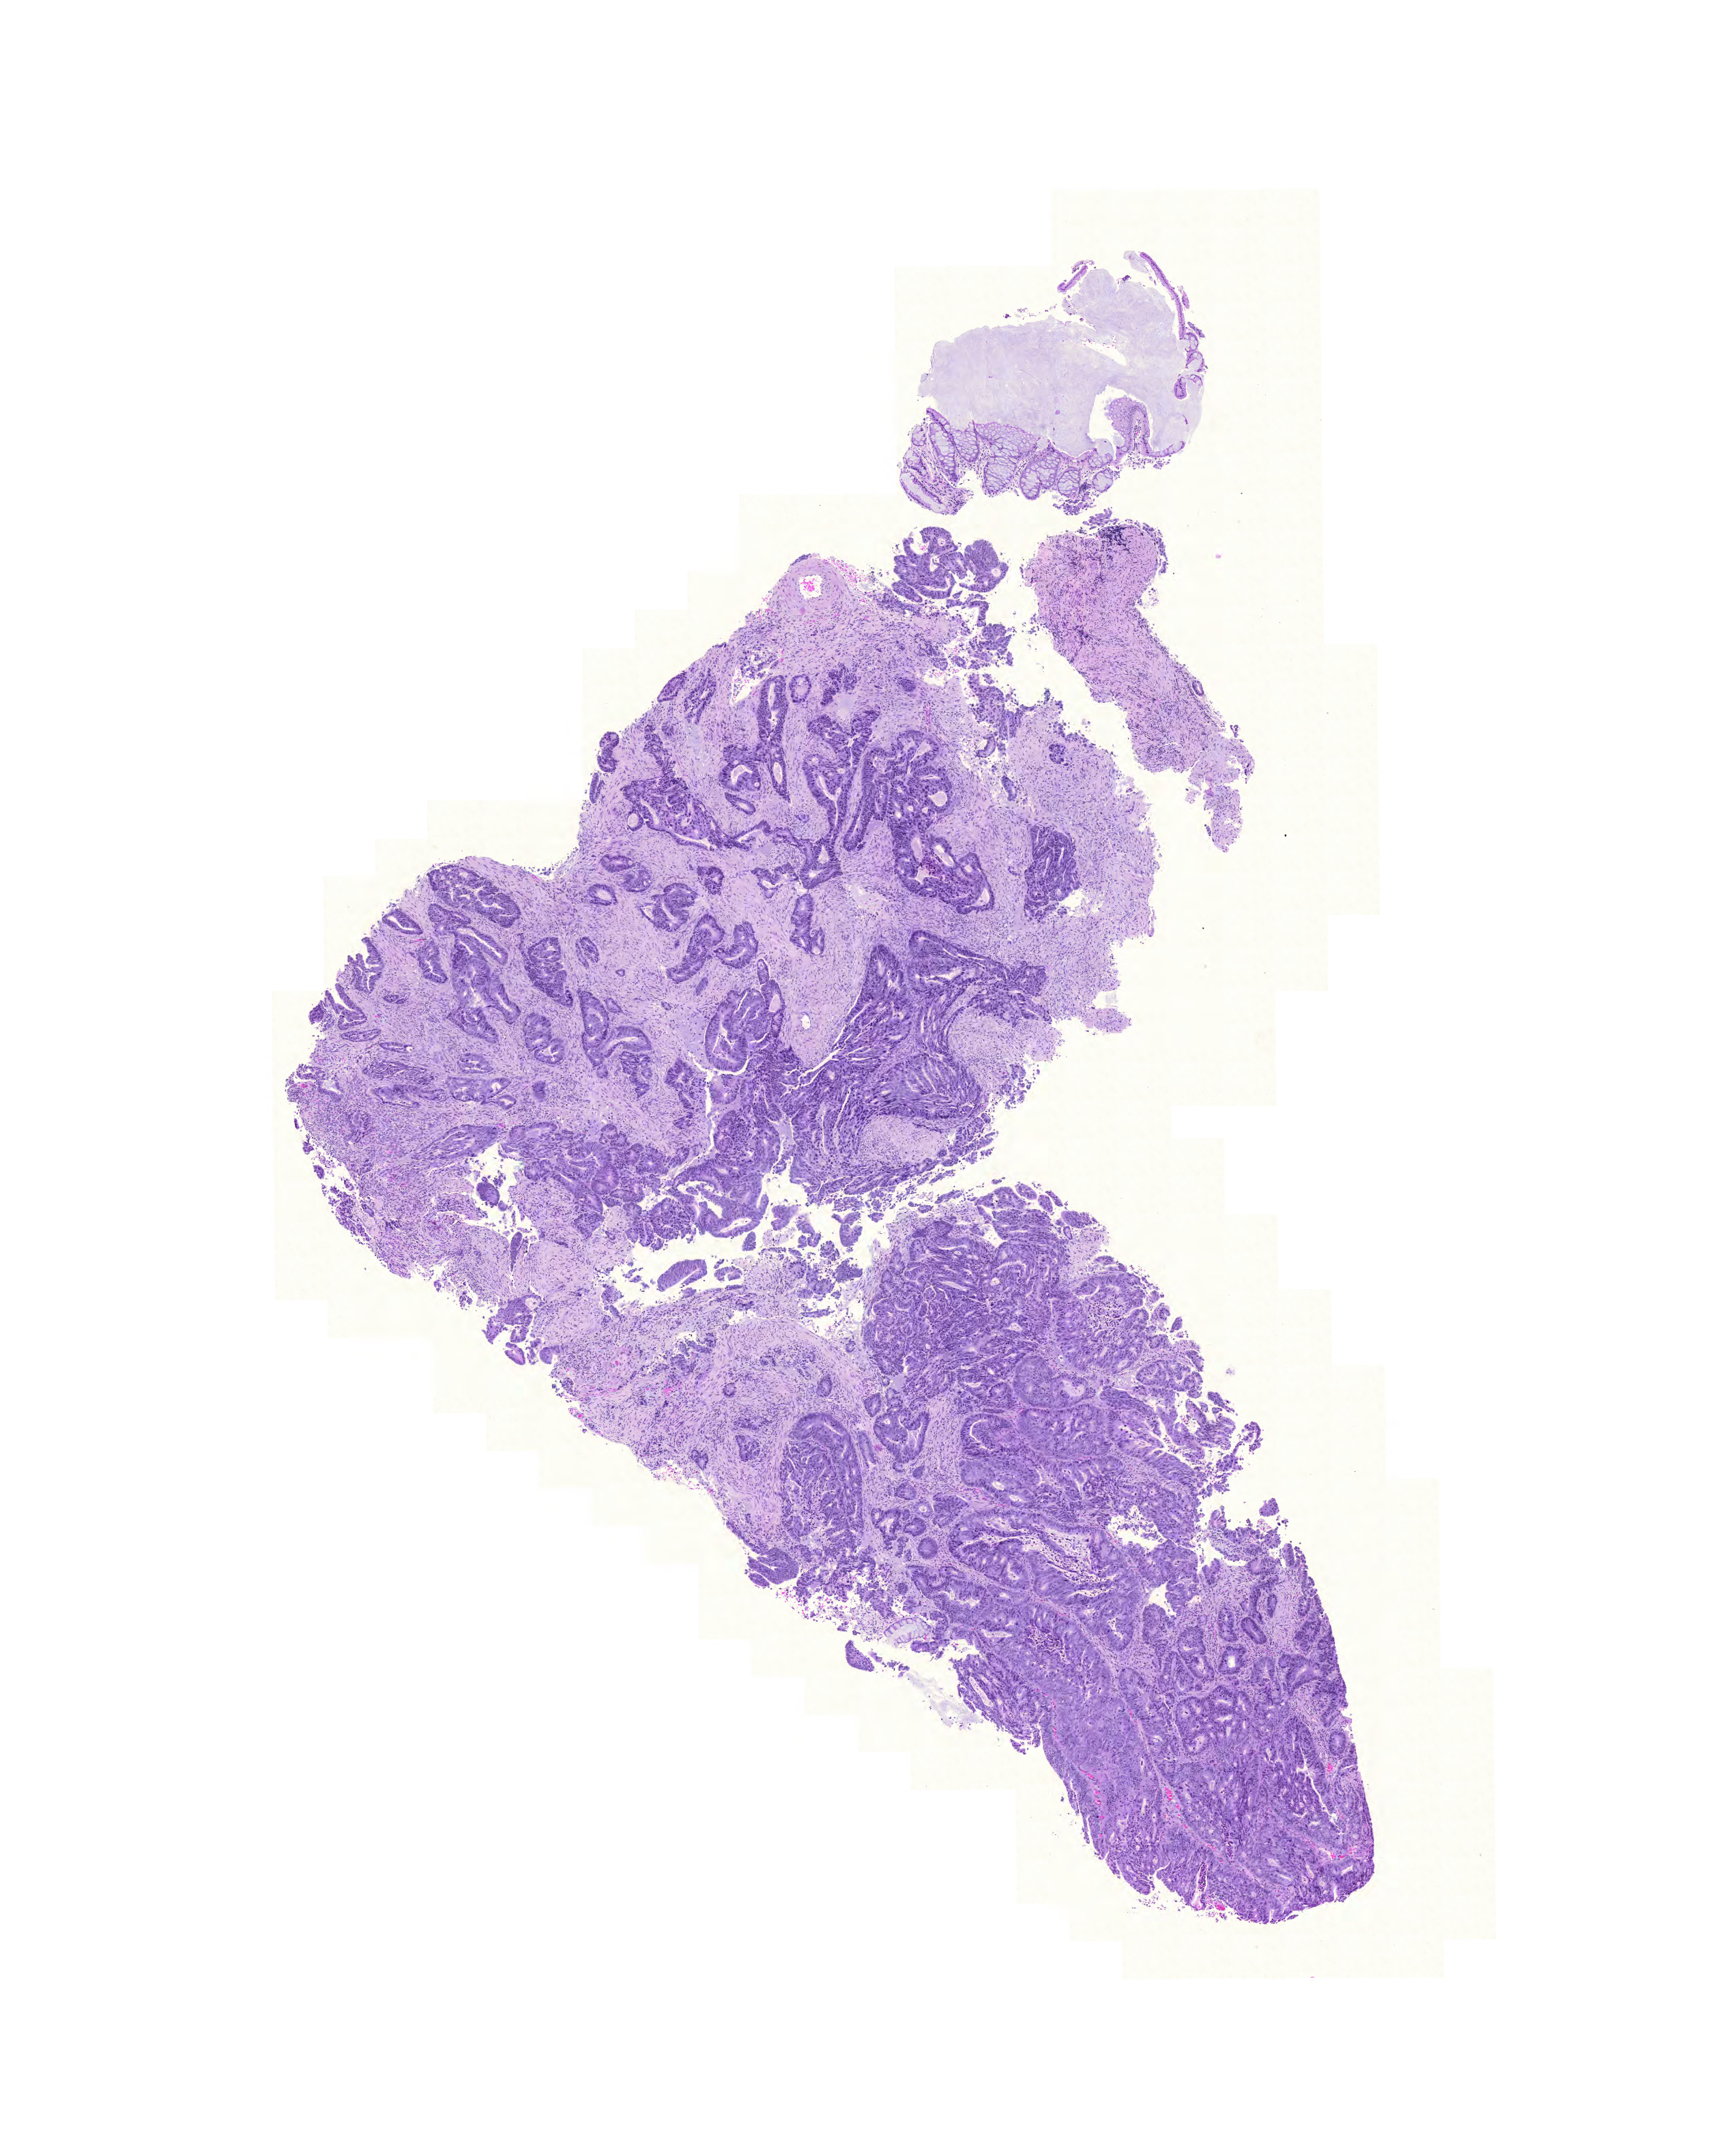
H&E whole-slide image — whole scanned area (about 9.5 x 11.6 mm) shown as a low-resolution overview. Formalin-fixed paraffin-embedded (FFPE) diagnostic section. Sample: primary tumour, colon. Male, age 70 years at initial diagnosis.
* AJCC pathologic stage: IIIA
* TNM: T2 N1 M0
* lymph nodes positive (case pathology): 2 of 16 examined
* diagnosis: Adenocarcinoma, NOS (rectosigmoid junction)